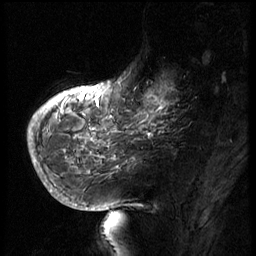
Breast MRI (dynamic contrast-enhanced), one sagittal slice; 3 images stored at this slice position (order not interpretable as contrast timing); 1.5 T; TE 4.2 ms, TR 8.9 ms; 2.5 mm slice thickness; 256 × 256 image matrix, field of view 200 × 200 mm. Patient: female, 56 years. From the clinical record (not read from this slice): setting: breast cancer imaged before/during neoadjuvant chemotherapy.
Annotated regions visible in this slice (semi-automatically segmented with operator editing):
- analysis volume of interest (the breast-tissue region the enhancement analysis was run in; not a lesion): bounding box (x1, y1, x2, y2) in pixels: (129, 62, 194, 127)
- tumour enhancement mask (voxels above the 140 % enhancement threshold inside the analysis volume of interest): (129, 84, 176, 127)